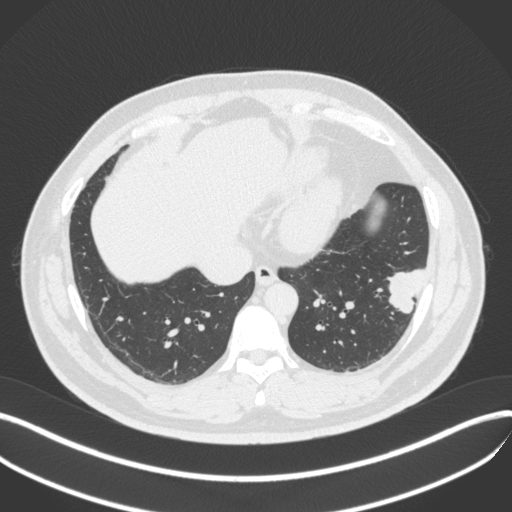
Chest CT, one axial slice. Slice 130 of 420 in the series (ordered by position). Lung window (W 1500 / L -600 HU). 512 × 512 image matrix, field of view 400 × 400 mm. Male patient, age 39 years. From the clinical record (not read from this slice): clinical TNM (as recorded): T2a N0 M0; histopathological grade: G2-3.
Outlined on this slice (bounding box drawn by a radiologist):
- lung tumour (recorded histology: adenocarcinoma): bounding box <383,261,431,321> (left, top, right, bottom; pixels)